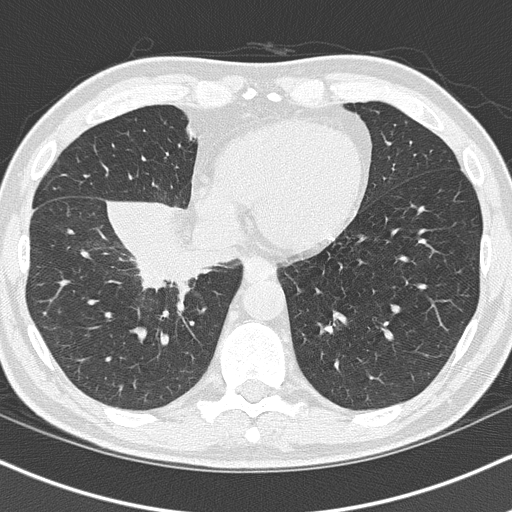
Low-dose screening chest CT, one axial slice. Position 37 of 151 along the scan axis. Reconstruction kernel B50f. 120 kVp. Lung window (W 1500 / L -600 HU). 512 × 512 image matrix, field of view 320 × 320 mm.
Annotated regions visible in this slice (manually delineated by an expert):
- lesion 1 (tumor, hilum of right lung): bounding box (x1, y1, x2, y2) in pixels: (136, 229, 201, 287)